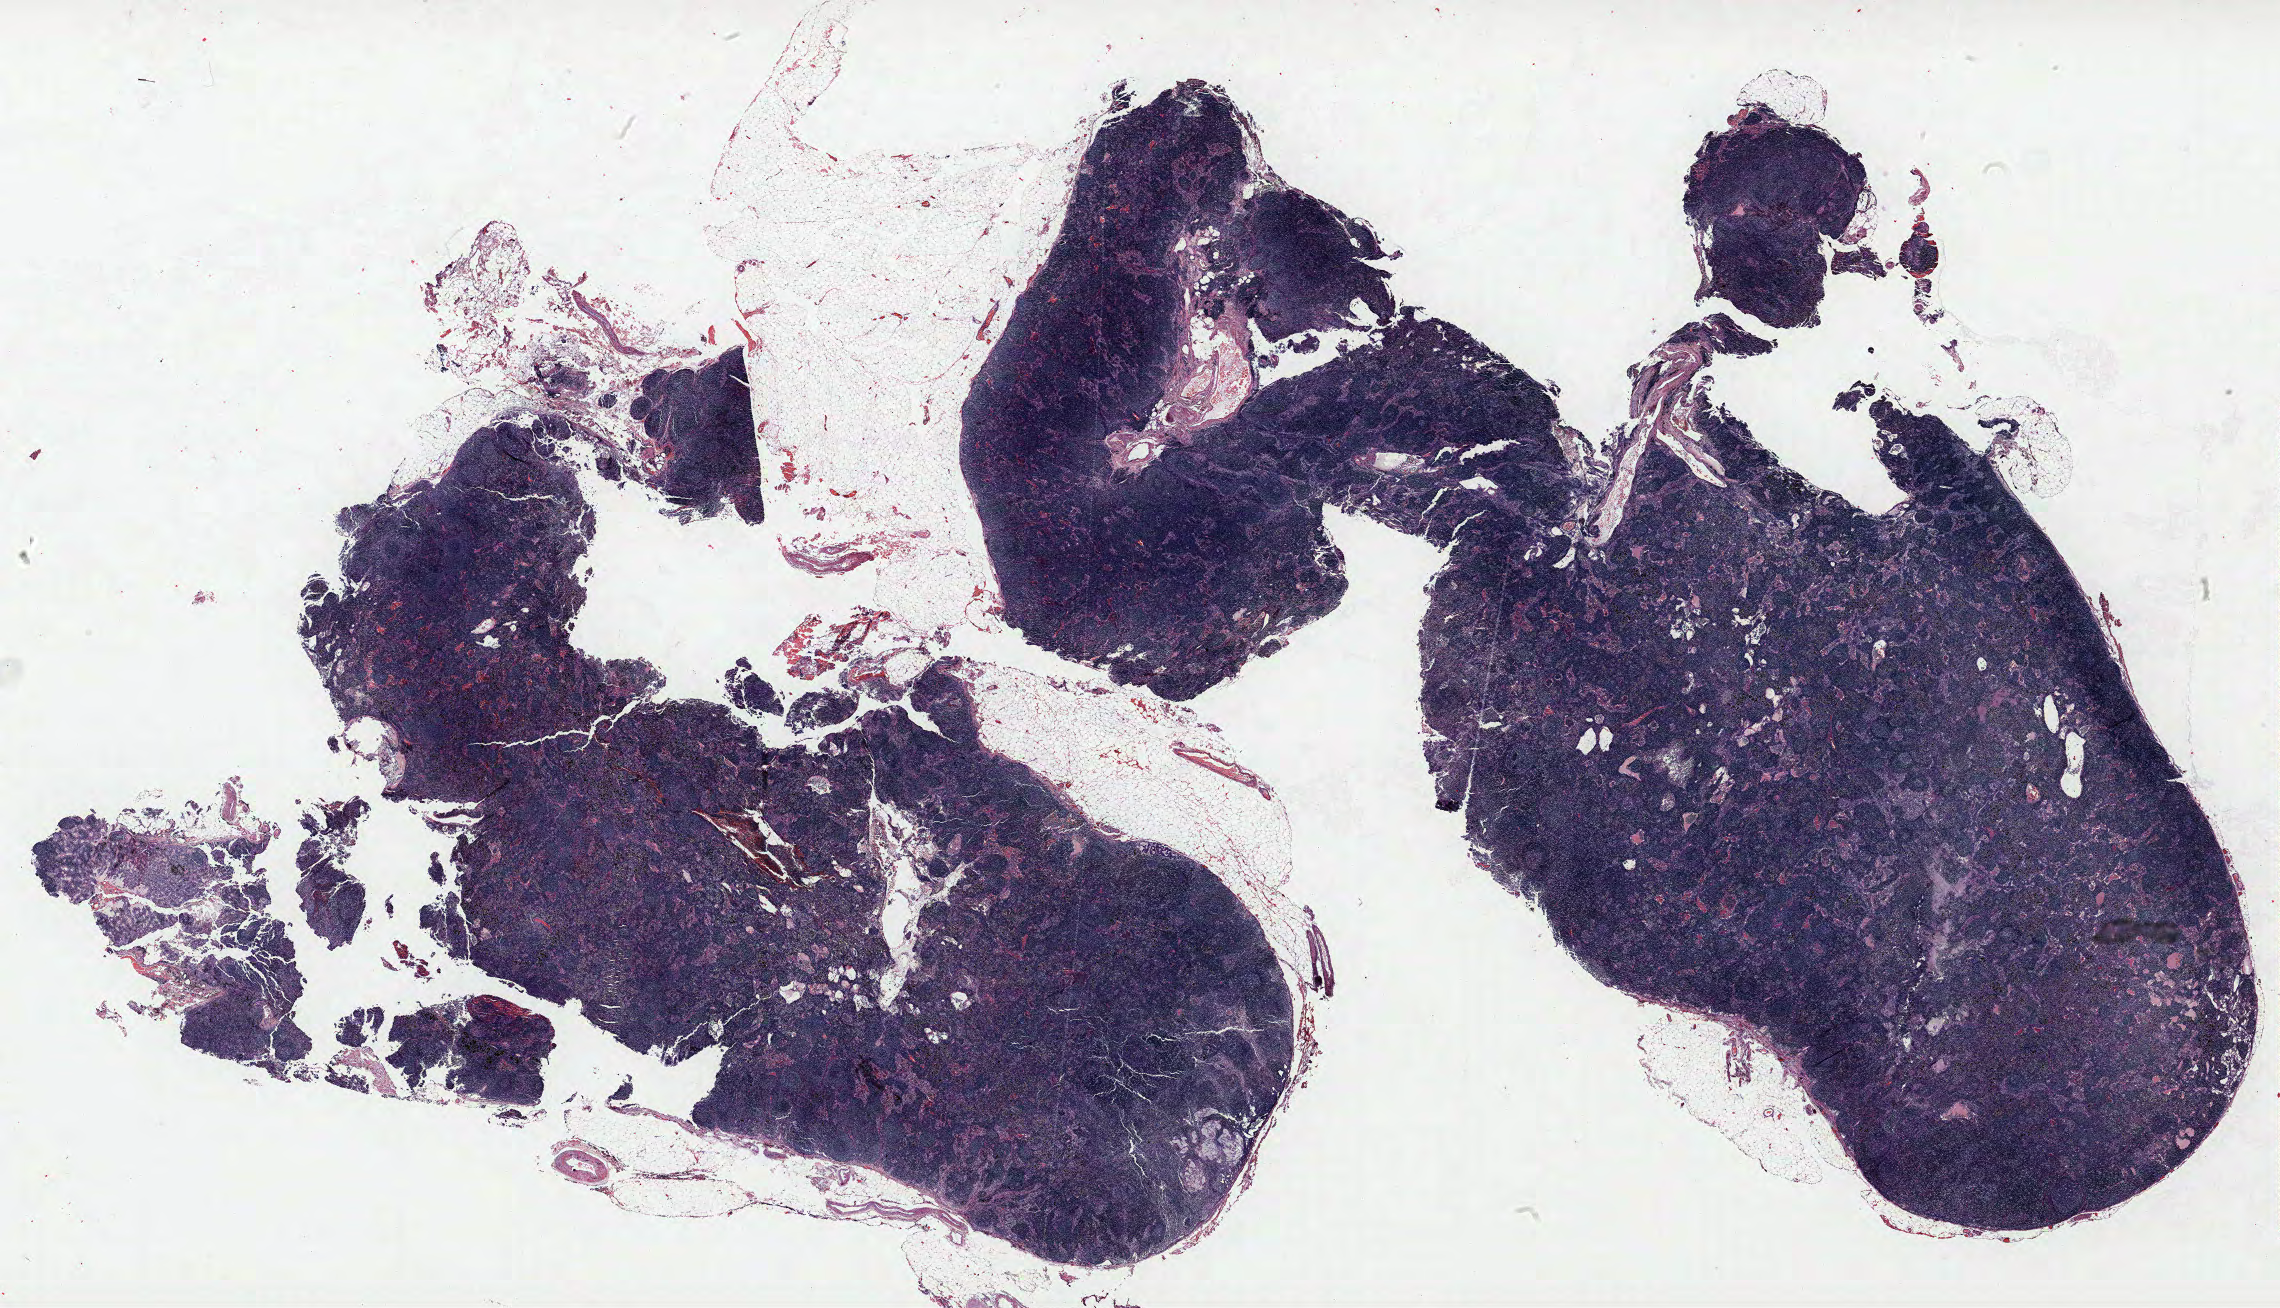
H&E-stained whole-slide image, whole scanned area (about 36.5 x 20.9 mm, slide scanned at 40x) shown as a low-resolution overview. FFPE section. Lung tissue. Female, age 73 at enrolment. Former smoker at enrolment. Grade: well differentiated (G1).
Tumour size (pathology): 85 mm. Primary tumour location (clinical record): right lower lobe. Stage (AJCC 6th edition): IV. ICD-O-3 topography: lower lobe of lung (C34.3). Participant's lung-cancer diagnosis: Mucinous adenocarcinoma.